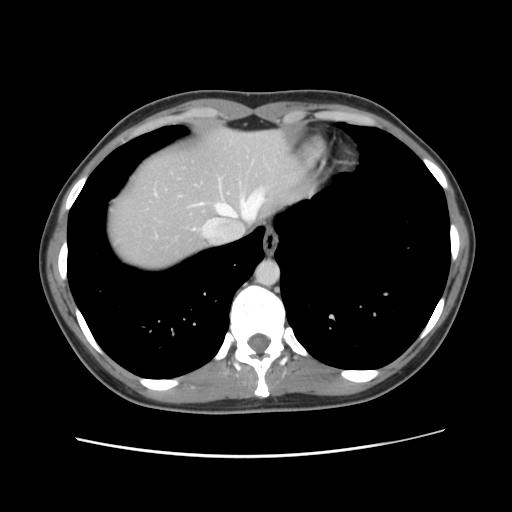
Contrast-enhanced abdominal CT, one axial slice. Slice 109 of 134 in the series (ordered by position). 120 kVp. Intravenous contrast given. Soft-tissue window (W 400 / L 40 HU). 2.5 mm slice thickness. 512 × 512 image matrix, field of view 339 × 339 mm. Female patient, age 33 years. From the clinical record (not read from this slice): diagnosis: colorectal cancer liver metastases, imaged before liver resection.
Outlined on this slice (manually delineated by an expert):
- hepatic veins: box from (x=195, y=190) to (x=264, y=237) px
- liver: (x=107, y=128)–(x=310, y=271)
- planned liver remnant (the part of the liver to remain after resection): (x=107, y=128)–(x=310, y=271)